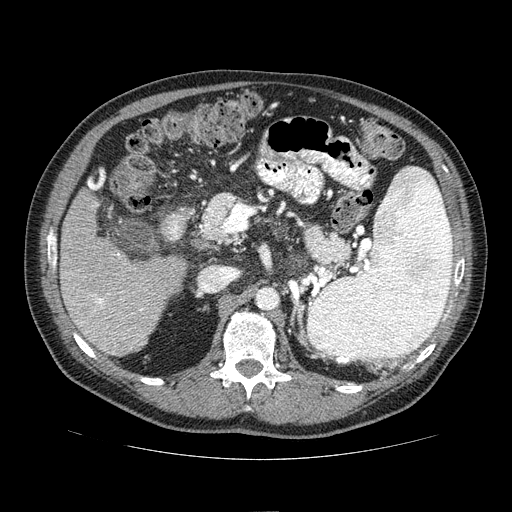
Contrast-enhanced abdominal CT (liver protocol), one axial slice; slice 30 of 81 in the series (ordered by position); reconstruction kernel STANDARD; one of 2 acquisitions stored at this slice position; soft-tissue window (W 400 / L 40 HU); 2.5 mm slice thickness; 512 × 512 image matrix. Case-level facts recorded for this patient, not image findings: diagnosis: hepatocellular carcinoma (patient treated with transarterial chemoembolisation; whether this scan precedes or follows treatment is not stated here); TNM stage (as recorded): Stage-IIIA; Child-Pugh class: A; tumour nodularity: multinodular; tumour size: 5.6 cm.
Structures marked on this image (semi-automatically segmented with operator editing):
- liver parenchyma outside the tumour (the mass and vessels are separate outlines, so this box may not span the whole liver): bounding box <60,178,186,356> (left, top, right, bottom; pixels)
- liver vessels: <82,180,143,339>